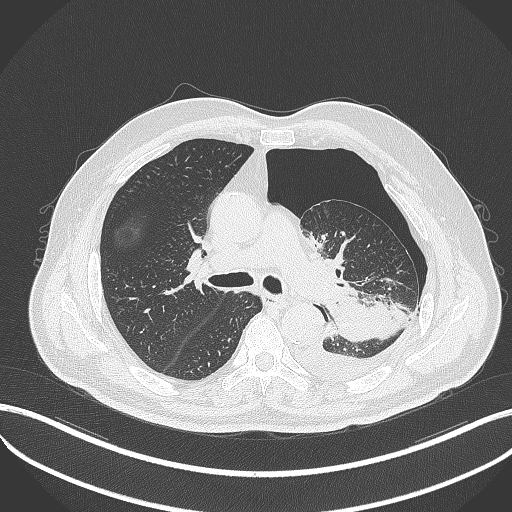
Chest CT, one axial slice. Position 322 of 464 along the scan axis. Lung window (W 1500 / L -600 HU). 1 mm slice thickness. 512 × 512 image matrix, field of view 400 × 400 mm. Patient: male, 76 years. Case-level facts recorded for this patient, not image findings: clinical TNM (as recorded): T3 N0 M1b.
Annotated regions visible in this slice (rectangle marked by the reading radiologist):
- lung tumour (recorded histology: adenocarcinoma): bounding box <326,284,405,345> (left, top, right, bottom; pixels)